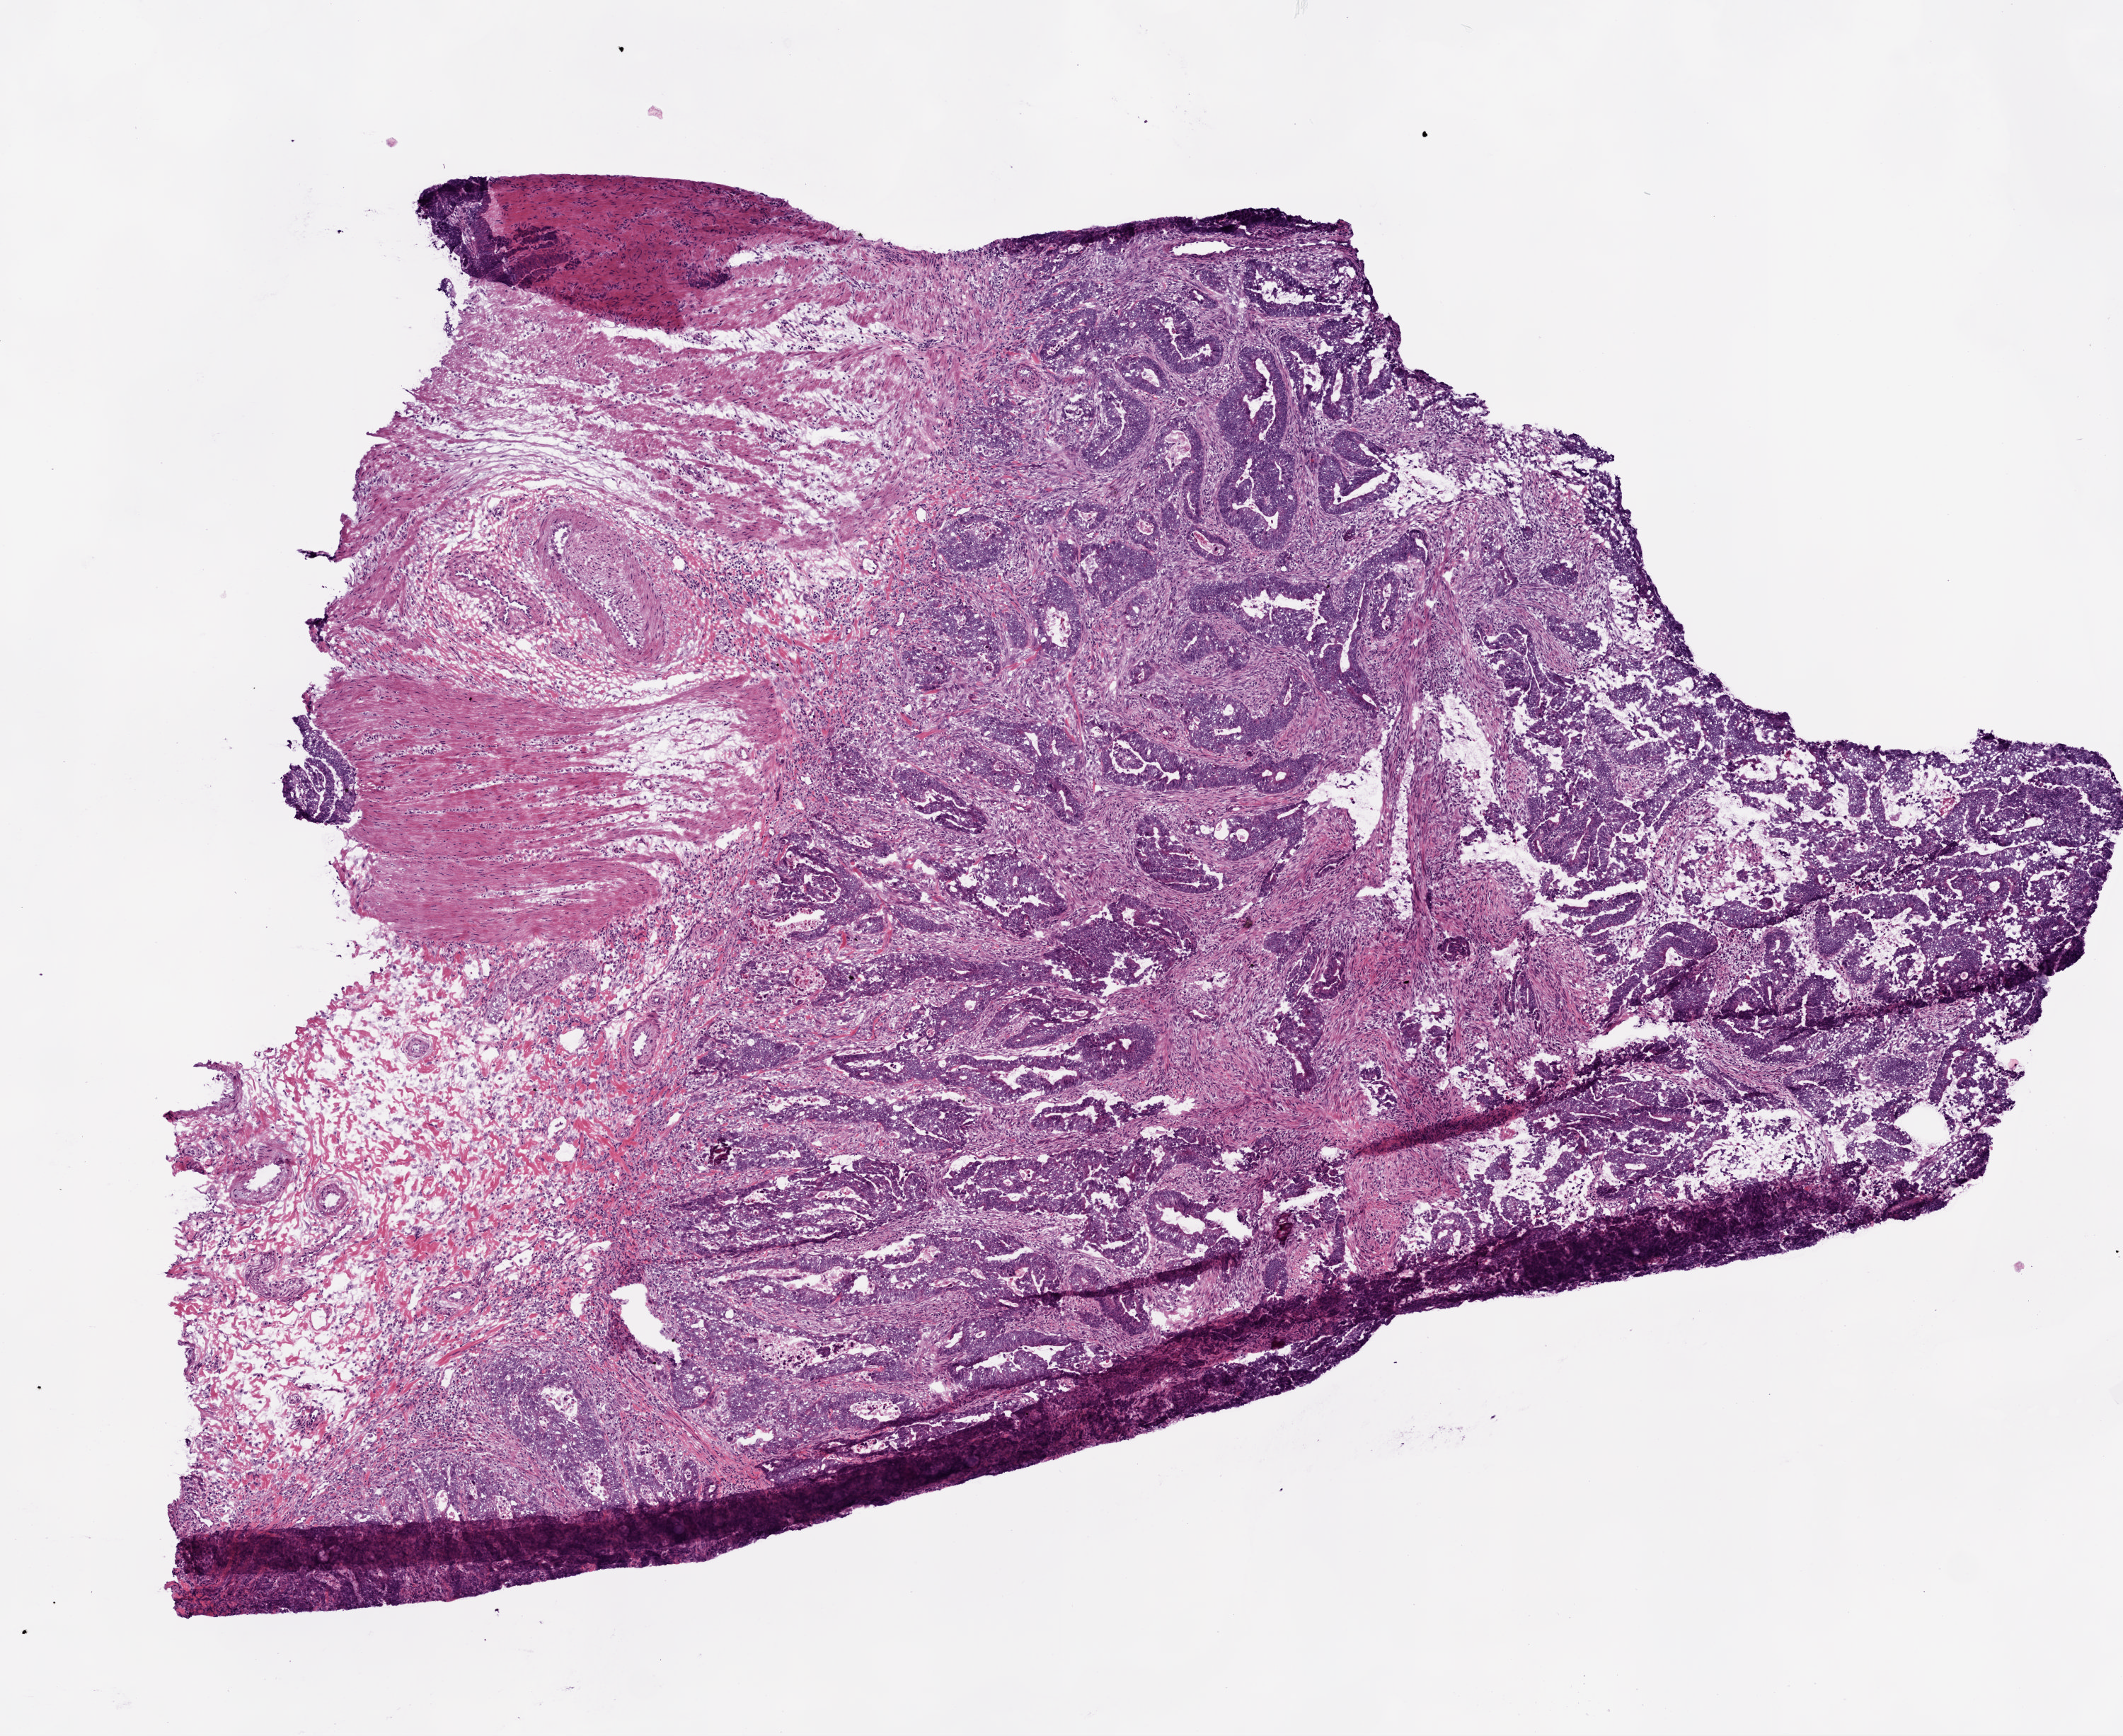
Digitized H&E-stained tissue section (whole slide) — low-resolution overview of the scanned area, about 6.0 x 4.9 mm (acquisition: 20x scan), frozen section, sample: primary tumour, colon. Female patient; age at initial diagnosis 40 years. Composition of this section per pathologist review: tumour cells 65%, tumour nuclei 60%, normal cells 30%, stromal cells 0%, necrosis 5%. Infiltration values recorded for this section: lymphocyte infiltration 20%, monocyte infiltration 1%, neutrophil infiltration 2%.
AJCC pathologic stage: IIIB (7th edition). Pathologic diagnosis: Adenocarcinoma, NOS (sigmoid colon). Lymph nodes positive (case pathology): 1 of 48 examined.